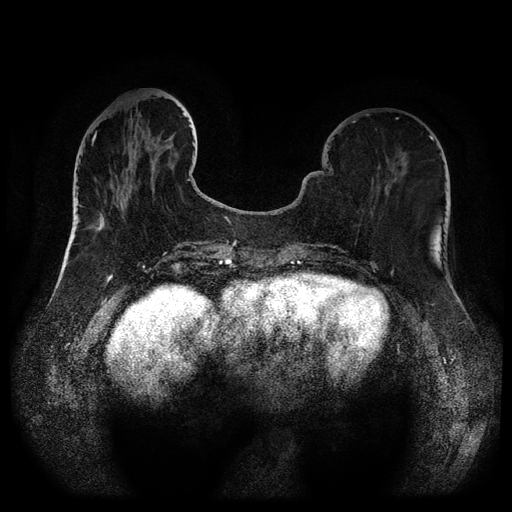
Breast MRI (dynamic contrast-enhanced, multi-phase), one axial slice. Slice 32 of 116 in the series (ordered by position). Dynamic contrast-enhanced series, time point 2 of 5 at this slice position (early post-contrast). 1.5 T. TE 2.6 ms, TR 5.3 ms. 512 × 512 image matrix. Patient: female, 75 years.
Annotated regions visible in this slice (semi-automatically segmented with operator editing):
- breast lesion (labelled benign in the annotation): bounding box (x1, y1, x2, y2) in pixels: (87, 210, 106, 235)